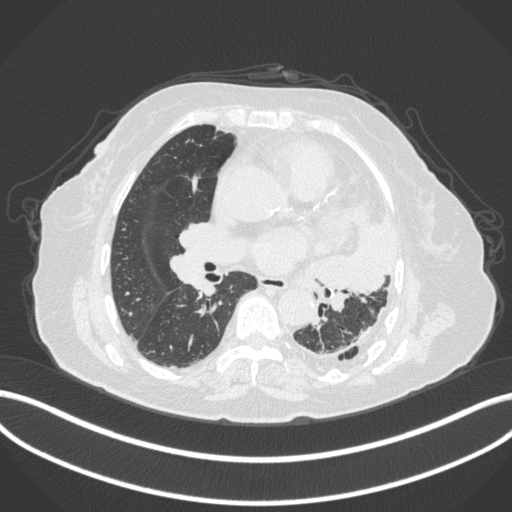
Chest CT, one axial slice. Position 189 of 399 along the scan axis. Reconstruction kernel B31f. 120 kVp. Lung window (W 1500 / L -600 HU). 512 × 512 image matrix, field of view 400 × 400 mm. Patient: female, 75 years. Case-level facts recorded for this patient, not image findings: clinical TNM (as recorded): T3 N3 M1.
Outlined on this slice (rectangle marked by the reading radiologist):
- lung tumour (recorded histology: adenocarcinoma): bounding box <309,199,394,314> (left, top, right, bottom; pixels)